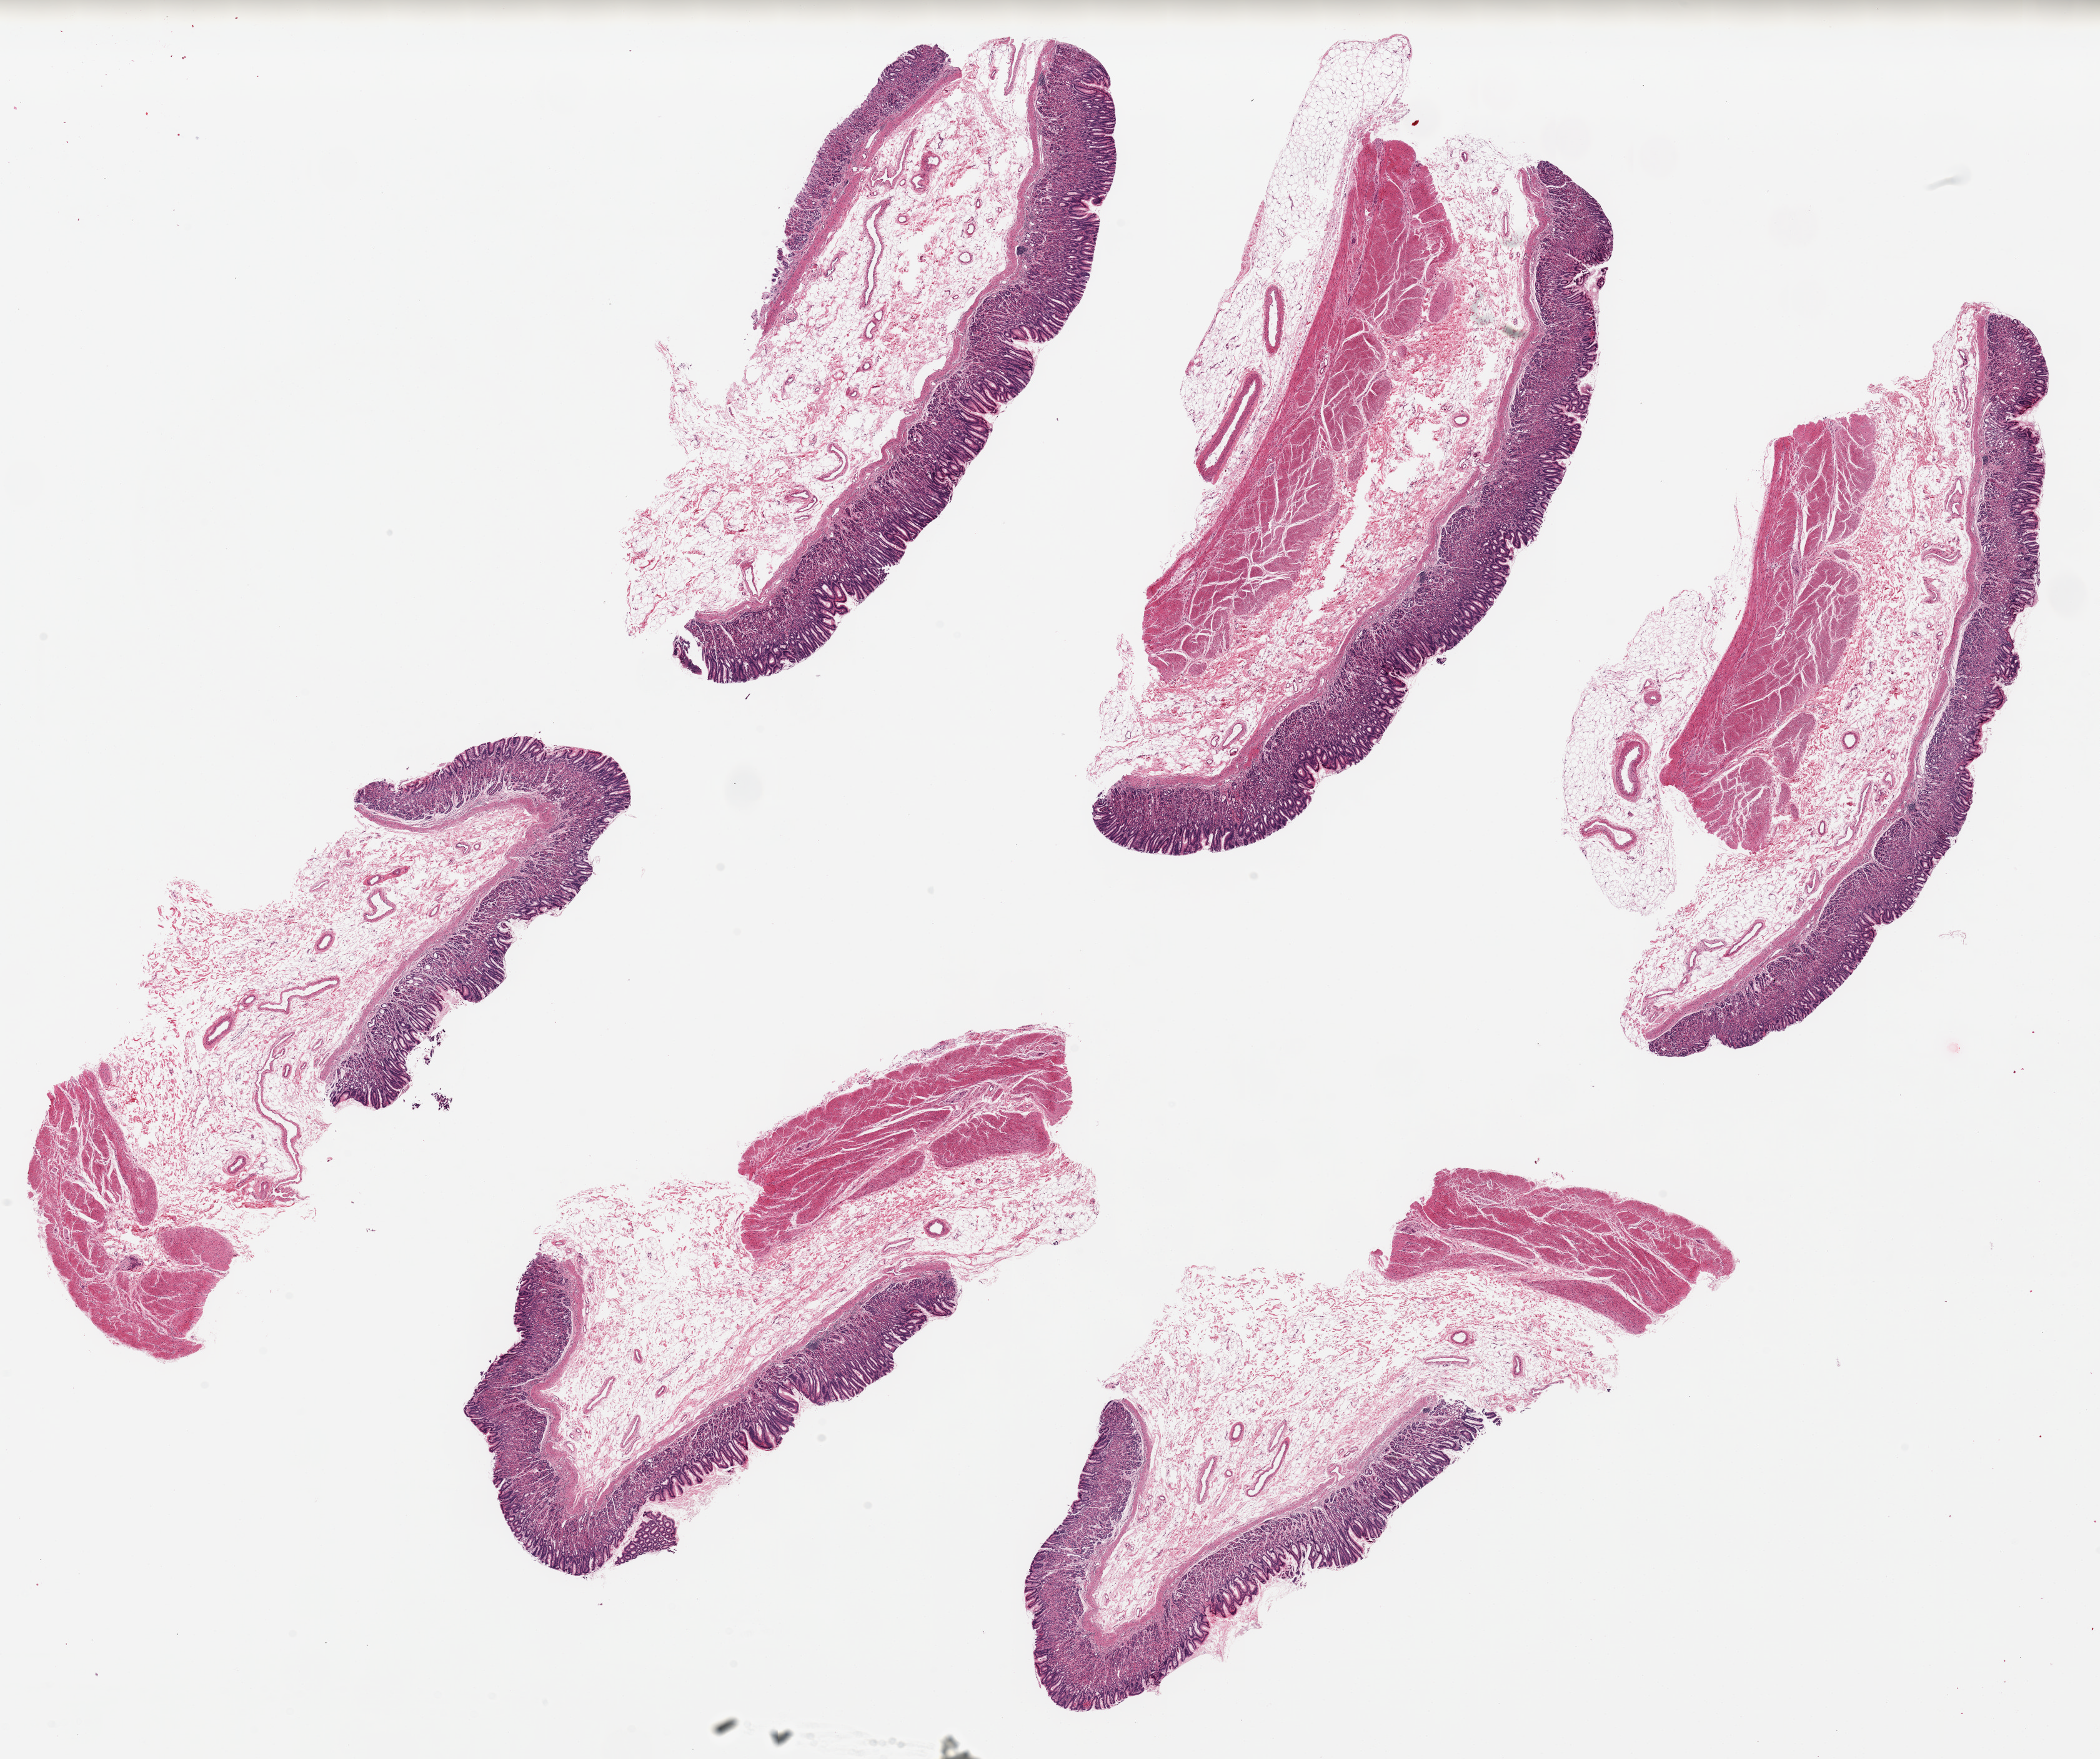
Hematoxylin and eosin (H&E) whole-slide image, whole scanned area (about 26.6 x 22.3 mm, slide scanned at 20x) shown as a low-resolution overview; PAXgene-fixed, paraffin-embedded tissue; section of stomach (target tissue); tissue donor sample. Male donor.
• review note (as recorded): 6 ~9.5x3.5mm pieces. Well-preserved mucosa is 20-30% of thickness